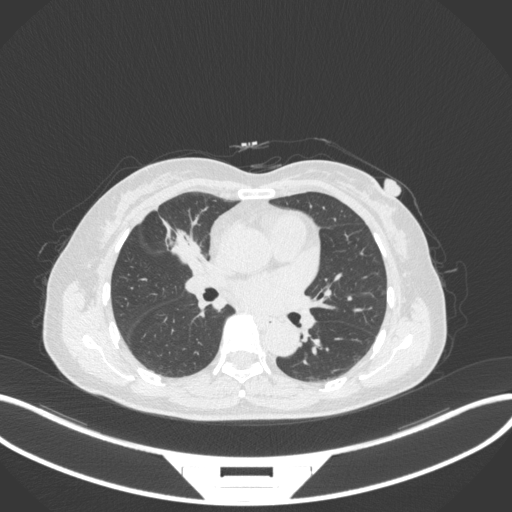
Chest CT, one axial slice; slice 159 of 282 in the series (ordered by position); reconstruction kernel B31f; 120 kVp; lung window (W 1500 / L -600 HU); 1 mm slice thickness; 512 × 512 image matrix, field of view 400 × 400 mm. Female patient, age 51 years. Case-level facts recorded for this patient, not image findings: clinical TNM (as recorded): T1c N0 M0; histopathological grade: G2.
Annotated regions visible in this slice (rectangle marked by the reading radiologist):
- lung tumour (recorded histology: adenocarcinoma): box from (x=169, y=223) to (x=204, y=265) px